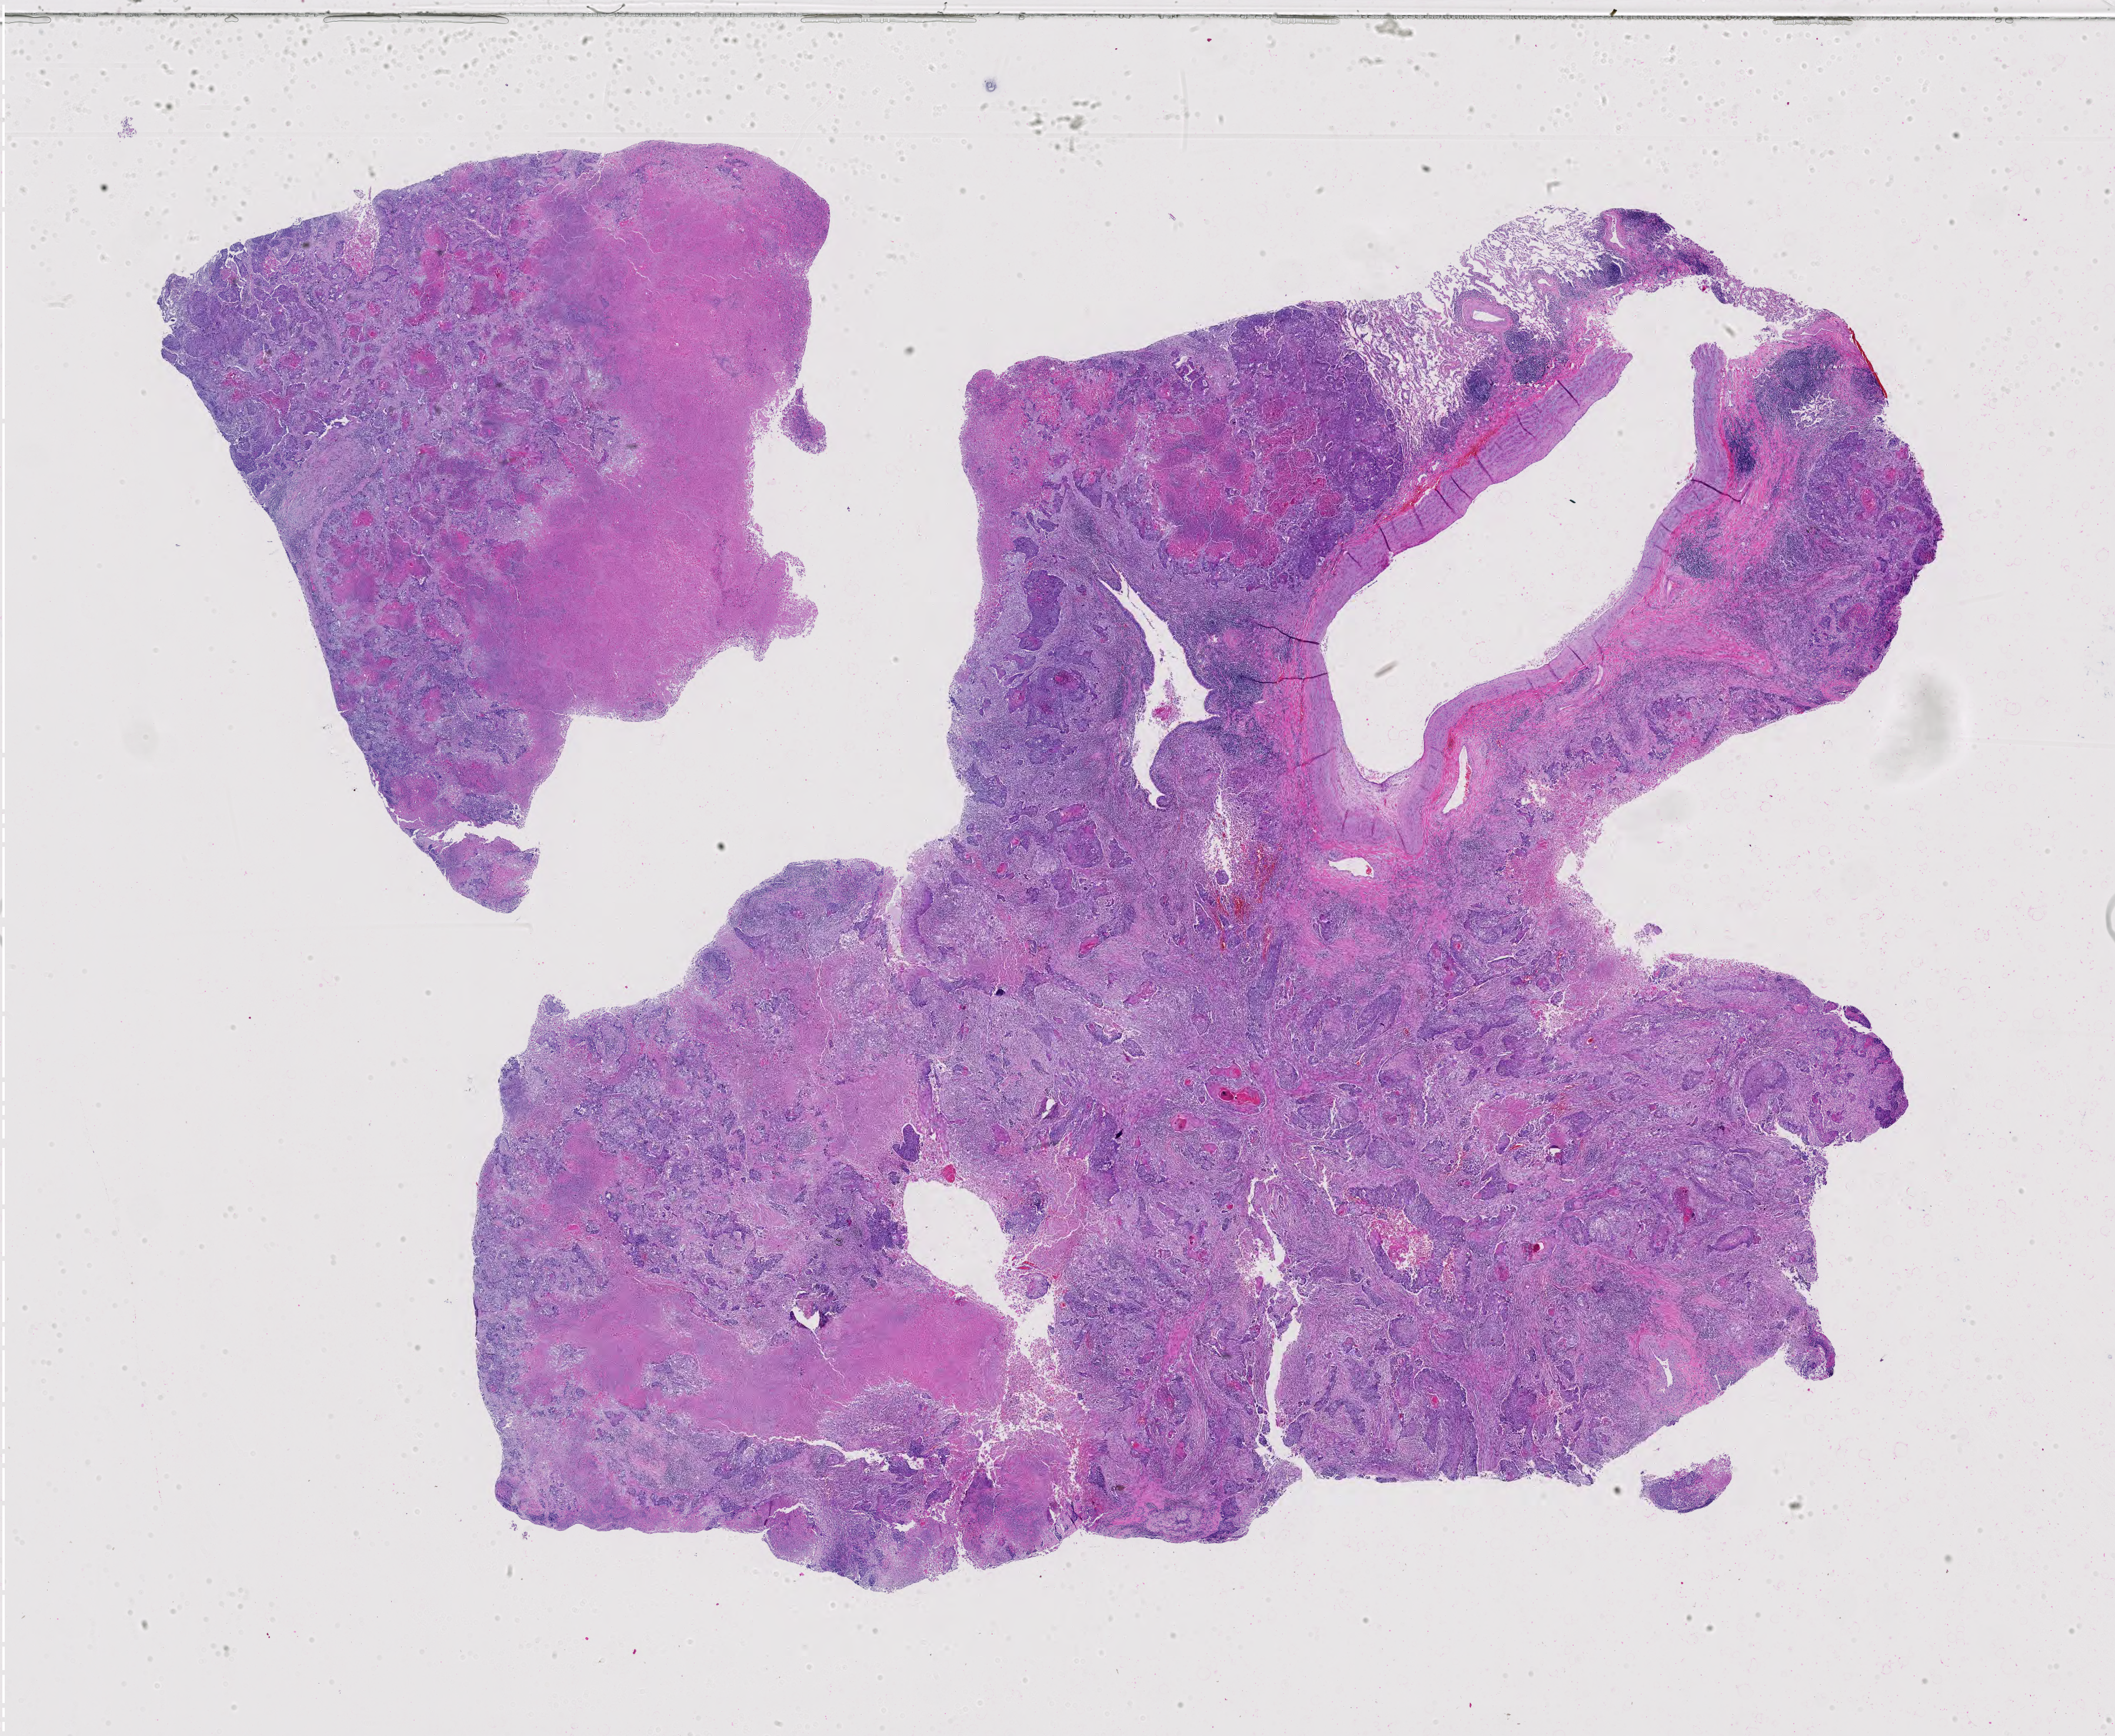
Whole-slide histology image, H&E — low-resolution overview of the scanned area, about 26.1 x 21.4 mm (acquisition: 40x scan), FFPE section, sample: primary tumour, lung. Male, age 62 years at initial diagnosis.
Diagnosis: Squamous cell carcinoma, NOS (lower lobe, lung).